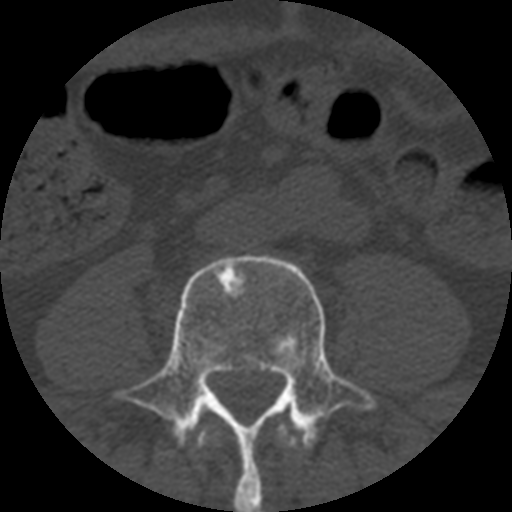
CT including the spine, one axial slice; slice 95 of 508 in the series (ordered by position); bone window (W 1800 / L 400 HU); 1.25 mm slice thickness; 512 × 512 image matrix. Patient age 57 years. Case-level facts recorded for this patient, not image findings: primary cancer: prostate.
Structures marked on this image (semi-automatic segmentation, software-assisted and operator-edited):
- L3 vertebra: bounding box [x1, y1, x2, y2] px = [196, 424, 298, 449]
- L4 vertebra: [114, 254, 376, 512]